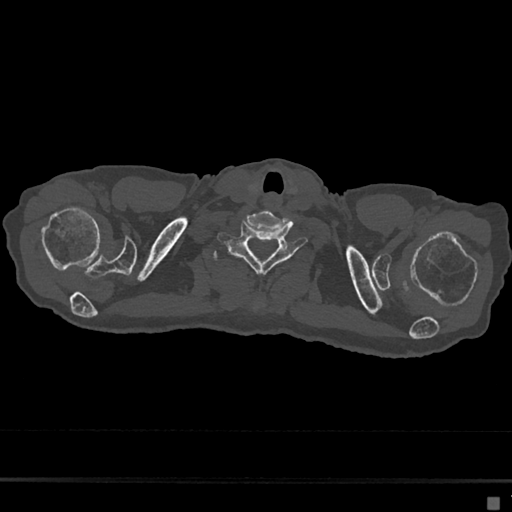
CT including the spine, one axial slice. Slice 636 of 797 in the series (ordered by position). 120 kVp. Bone window (W 1800 / L 400 HU). 0.5 mm slice thickness. 512 × 512 image matrix, field of view 360 × 360 mm. Patient: female, 68 years. Case-level facts recorded for this patient, not image findings: primary cancer: renal.
Structures marked on this image (semi-automatic segmentation, software-assisted and operator-edited):
- T1 vertebra: box from (x=213, y=251) to (x=219, y=262) px